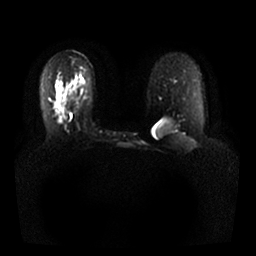
Breast MRI, one axial slice; position 18 of 25 along the scan axis; diffusion-weighted series; image 2 of 4 stored at this slice position (different b-values; order by instance number); 1.5 T; 4 mm slice thickness; 256 × 256 image matrix. Female patient.
Annotated regions visible in this slice (outlined manually by an expert reader):
- tumour on diffusion-weighted imaging: bounding box <57,107,65,120> (left, top, right, bottom; pixels)